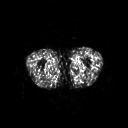
FDG PET of an extremity soft-tissue mass (from a PET/CT study), one axial slice; slice 227 of 311 in the series (ordered by position); 3.27 mm slice thickness; 128 × 128 image matrix. Male patient, age 29 years. From the clinical record (not read from this slice): histological type: mixoid liposarcoma; grade: low; site of the primary tumour: left thigh.
Structures marked on this image (expert contour drawn on MRI and transferred to this co-registered scan by the dataset authors):
- gross tumour volume (mass): bounding box (x1, y1, x2, y2) in pixels: (74, 59, 79, 64)